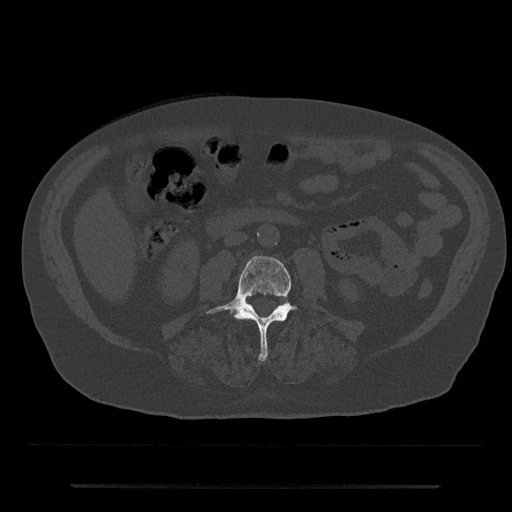
CT including the spine, one axial slice; position 407 of 797 along the scan axis; 120 kVp; bone window (W 1800 / L 400 HU); 0.5 mm slice thickness; 512 × 512 image matrix, field of view 434 × 434 mm. Male patient, age 80 years. From the clinical record (not read from this slice): primary cancer: prostate.
Outlined on this slice (semi-automatic segmentation, software-assisted and operator-edited):
- L3 vertebra: bounding box [x1, y1, x2, y2] px = [207, 256, 297, 362]